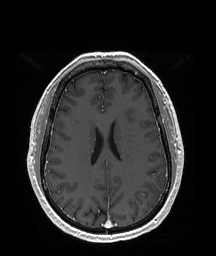
Brain MRI from a brain-tumour surgery series, one axial slice. T1-weighted post-contrast. 1 mm slice thickness. 216 × 256 image matrix, field of view 219 × 260 mm. Case-level facts recorded for this patient, not image findings: histopathology: Glioblastoma; WHO grade: 4; IDH mutation: no.
Annotated regions visible in this slice (expert manual segmentation):
- tumour: bounding box <142,181,164,208> (left, top, right, bottom; pixels)